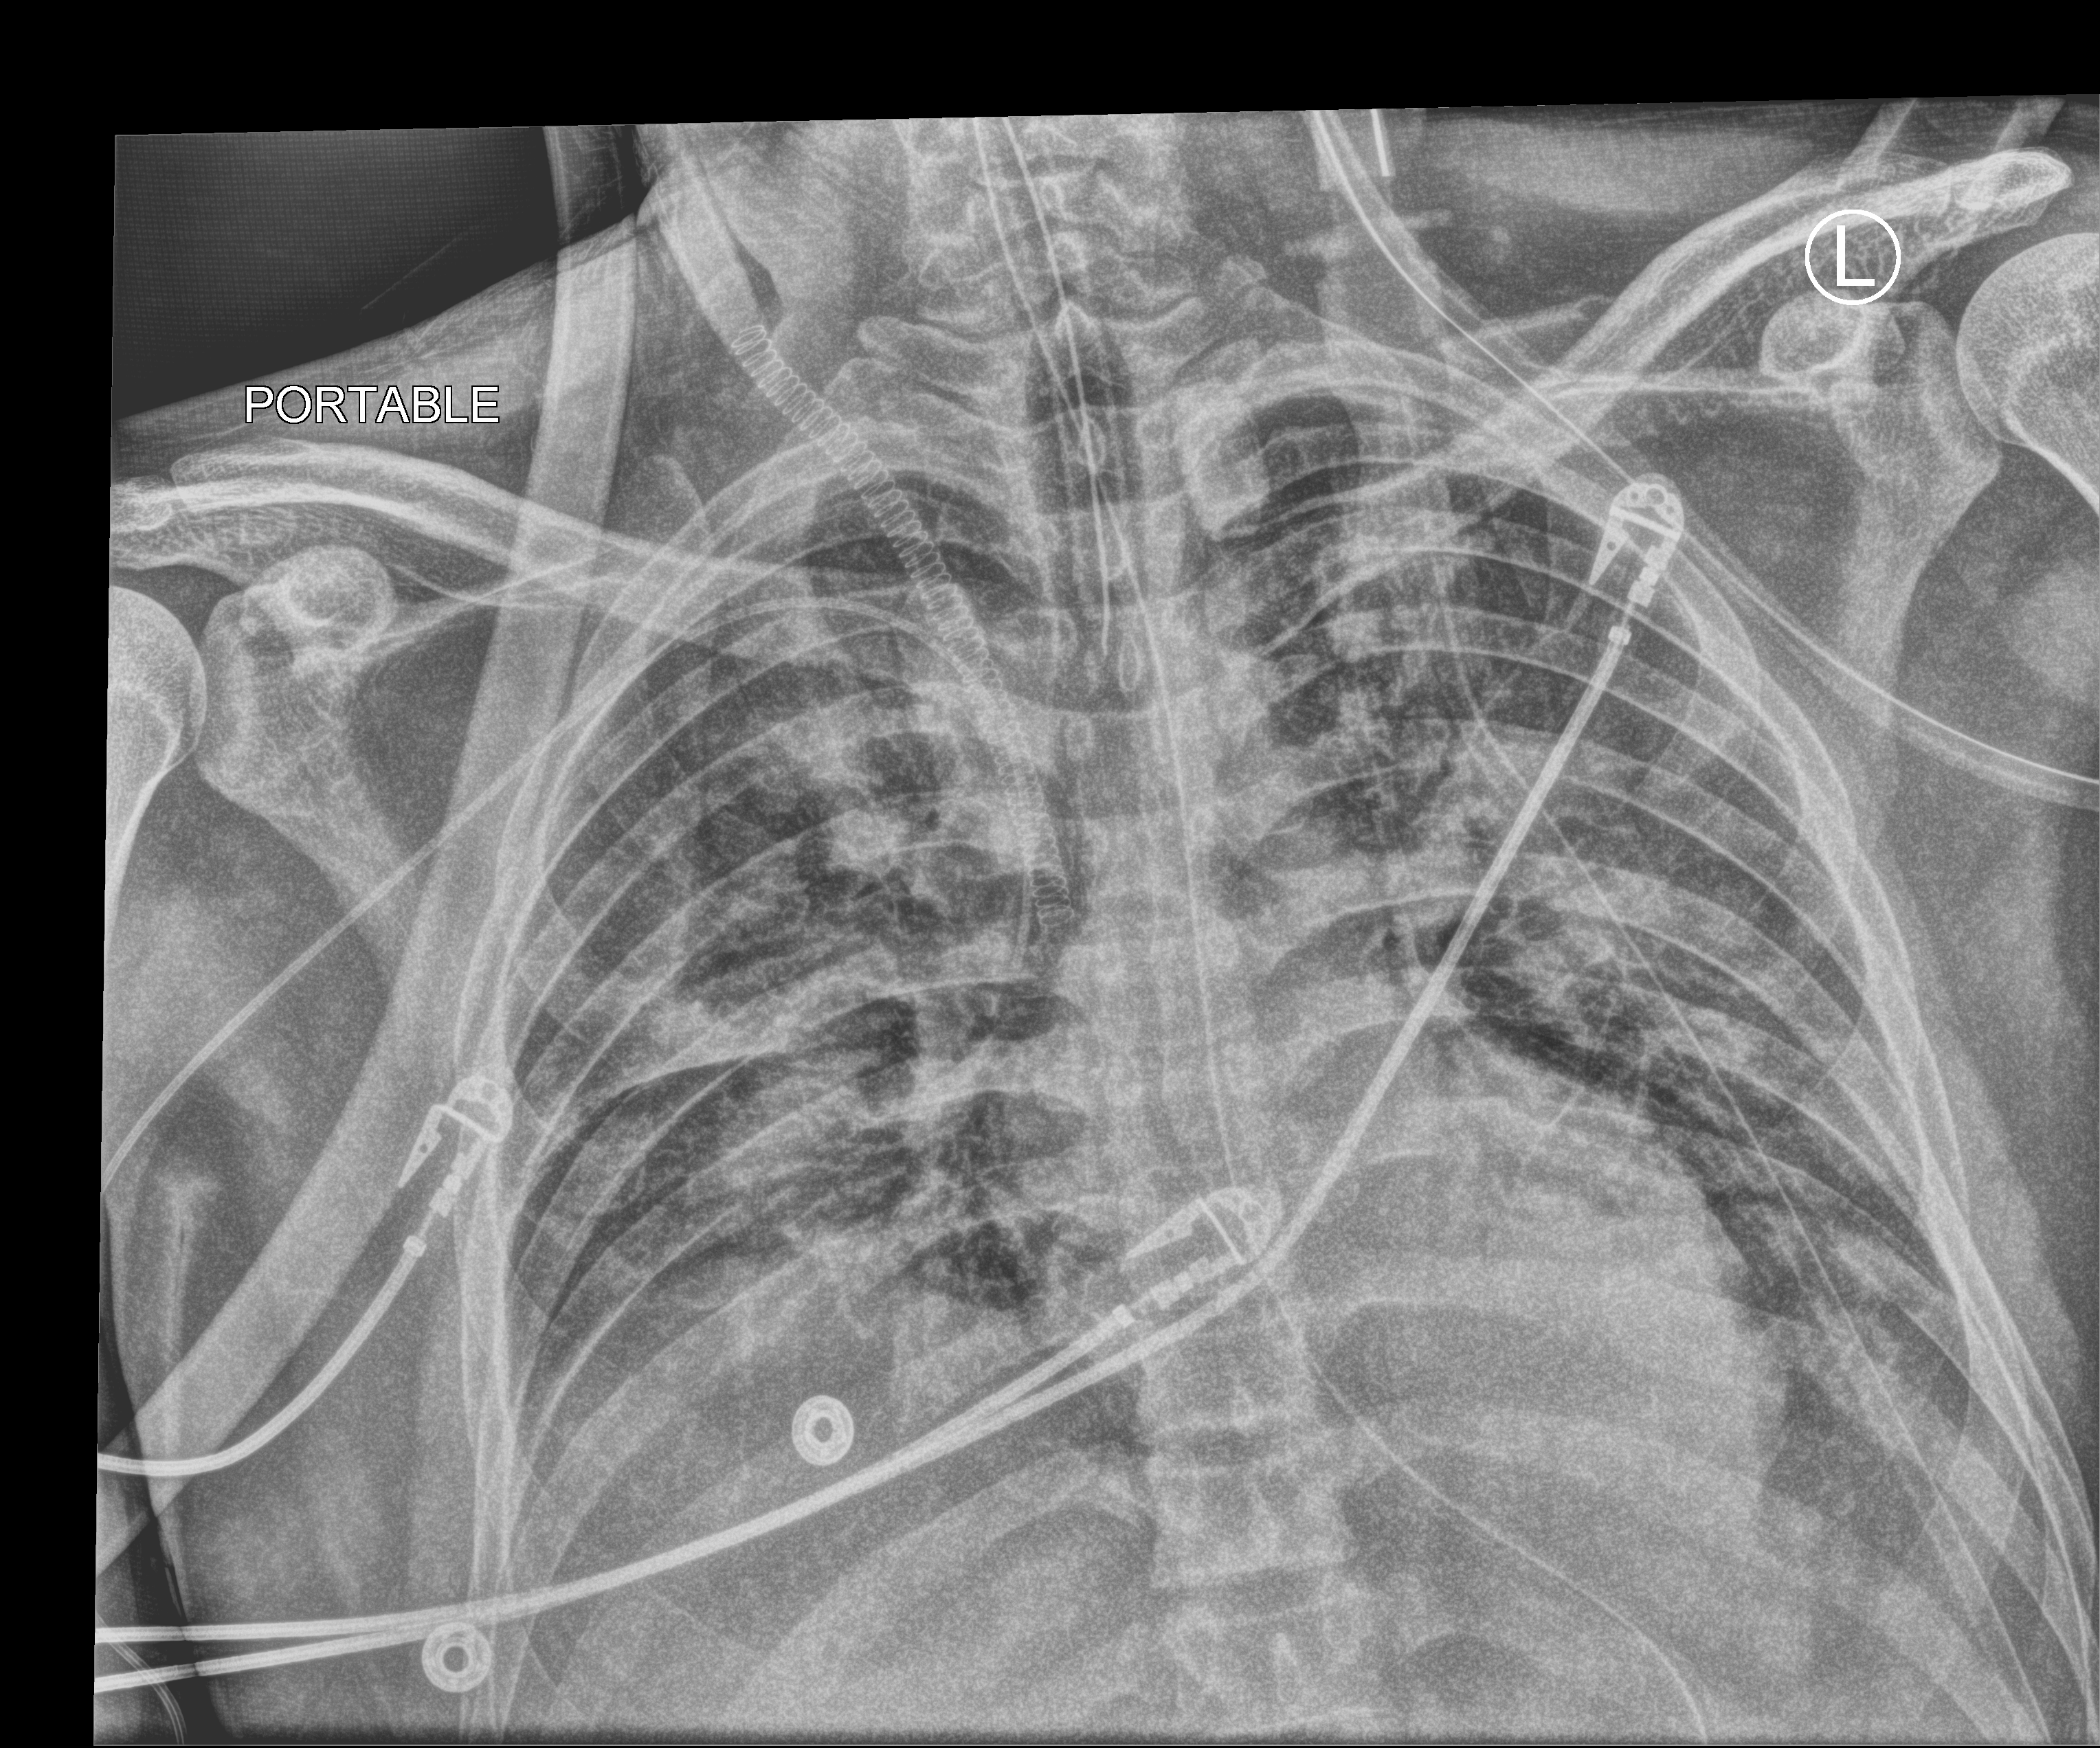
Bedside chest radiograph (computed radiography), anteroposterior (AP) projection. Patient hospitalised with COVID-19, aged 18–59 years.
From the hospital-stay record, not from the radiograph (when in the stay this image was taken is not recorded):
- smoking status (admission record): never